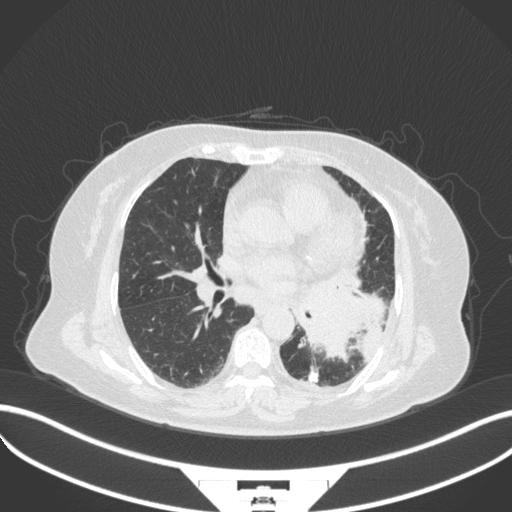
Chest CT, one axial slice. Position 172 of 328 along the scan axis. Reconstruction kernel B31f. Lung window (W 1500 / L -600 HU). 1 mm slice thickness. 512 × 512 image matrix, field of view 400 × 400 mm. Female patient, age 69 years. Case-level facts recorded for this patient, not image findings: clinical TNM (as recorded): T2b N3 M1.
Outlined on this slice (bounding box drawn by a radiologist):
- lung tumour (recorded histology: adenocarcinoma): bounding box (x1, y1, x2, y2) in pixels: (293, 278, 390, 367)